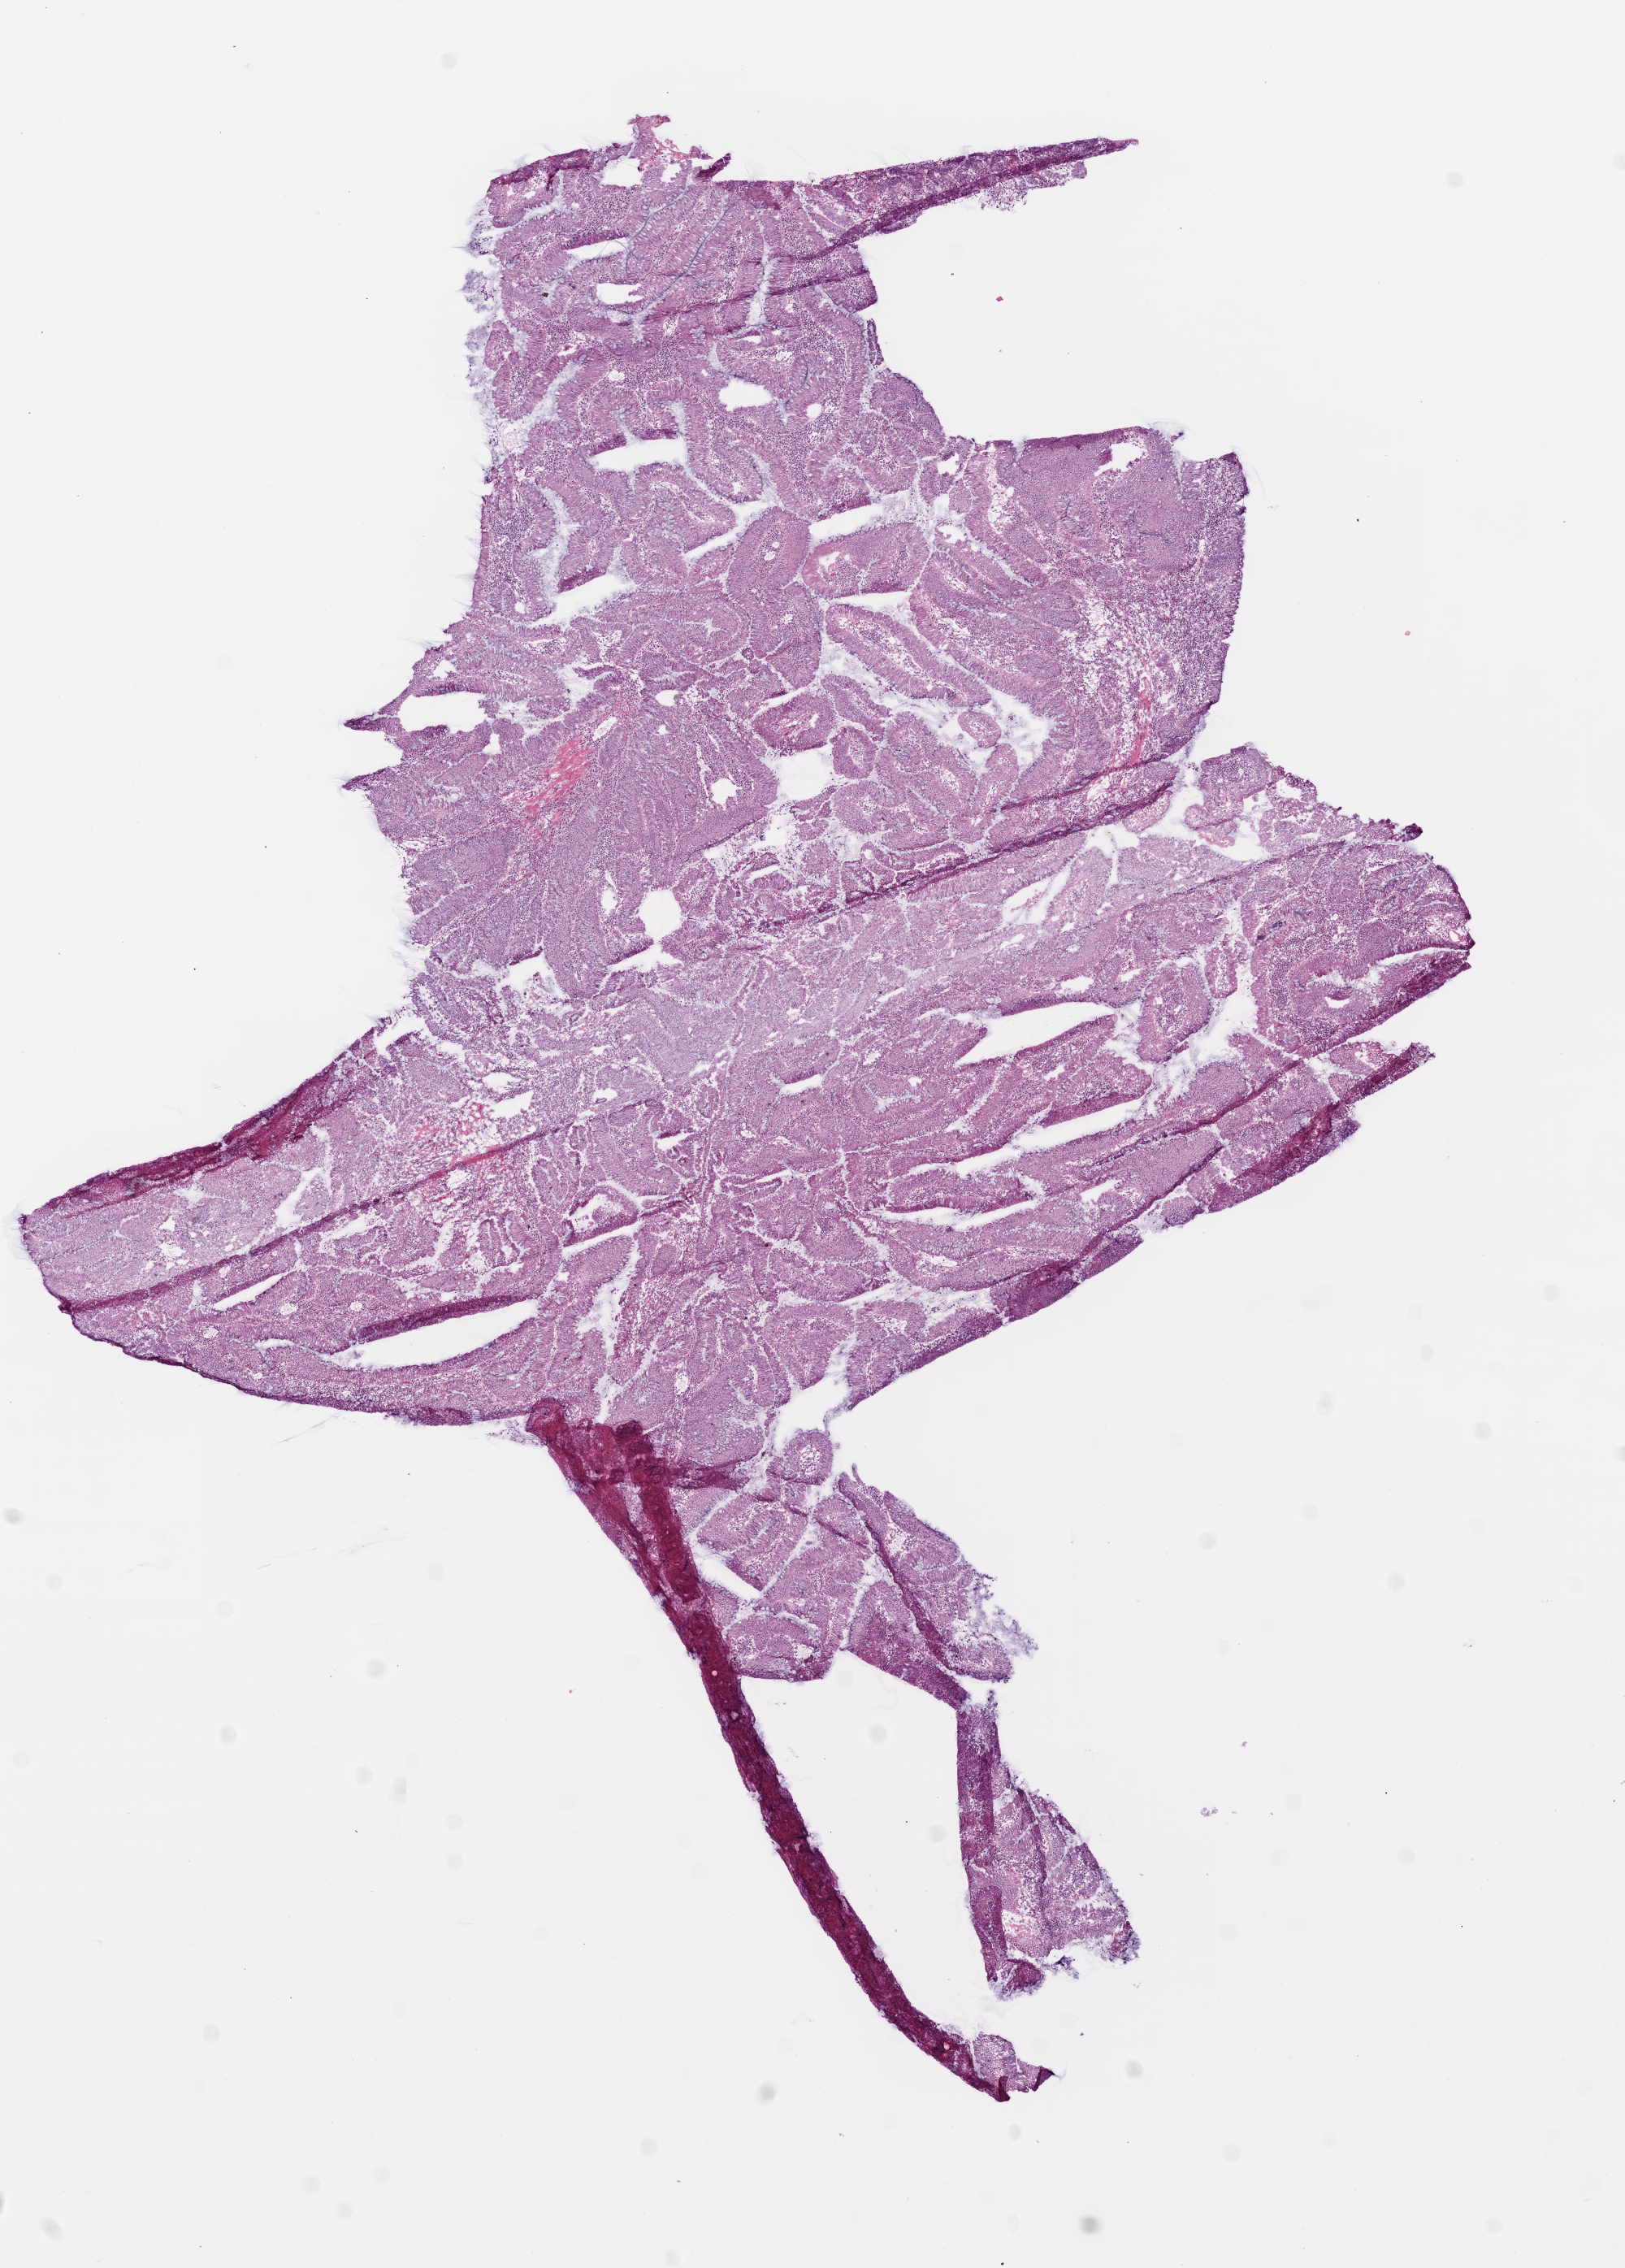
H&E whole-slide image — shown as a low-resolution overview of the whole scanned area (about 8.0 x 11.2 mm, acquisition: 20x scan). Frozen section. Primary tumour sample from the colon. Male, age 72 years at initial diagnosis. Pathologist review of this section (percent, as recorded): tumour cells 95%, tumour nuclei 80%, normal cells 0%, stromal cells 5%, necrosis 0%.
• AJCC pathologic stage: IIA (6th edition)
• diagnosis: Adenocarcinoma, NOS
• lymph nodes positive (case pathology): 0 of 17 examined